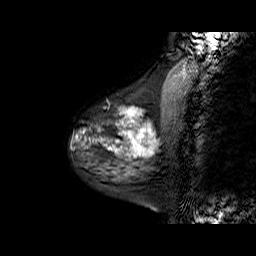
Breast MRI (dynamic contrast-enhanced), one sagittal slice; position 16 of 60 along the scan axis; dynamic contrast-enhanced series, time point 2 of 6 at this slice position (early post-contrast); 1.5 T; TE 6.3 ms, TR 32.9 ms; 4 mm slice thickness; 256 × 256 image matrix. Female patient. From the clinical record (not read from this slice): setting: breast cancer imaged before/during neoadjuvant chemotherapy; receptor status: HR-positive, HER2-negative.
Outlined on this slice (semi-automatic segmentation, software-assisted and operator-edited):
- analysis volume of interest (the breast-tissue region the enhancement analysis was run in; not a lesion): bounding box <77,86,169,170> (left, top, right, bottom; pixels)
- tumour enhancement mask (voxels above the 100 % enhancement threshold inside the analysis volume of interest): <109,107,152,156>